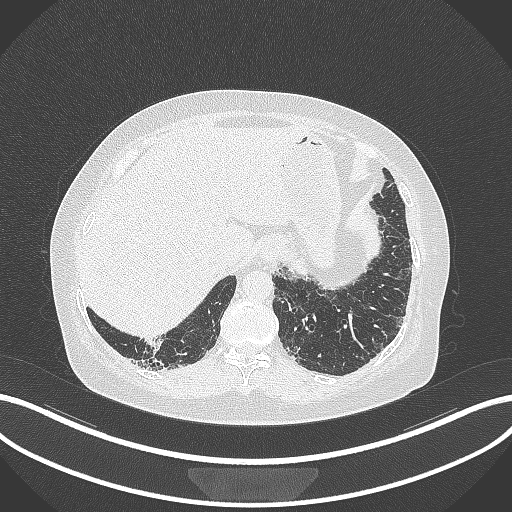
Chest CT, one axial slice; position 8 of 296 along the scan axis; lung window (W 1500 / L -600 HU); 1 mm slice thickness; 512 × 512 image matrix, field of view 400 × 400 mm. Female patient, age 65 years. Case-level facts recorded for this patient, not image findings: clinical TNM (as recorded): T2b N1 M0; histopathological grade: G1.
Structures marked on this image (bounding box drawn by a radiologist):
- lung tumour (recorded histology: adenocarcinoma): bounding box (x1, y1, x2, y2) in pixels: (138, 329, 165, 357)